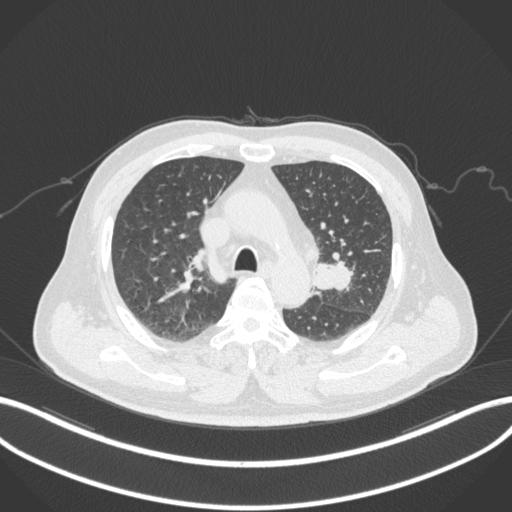
Chest CT, one axial slice. Slice 207 of 286 in the series (ordered by position). Reconstruction kernel B31f. 120 kVp. Lung window (W 1500 / L -600 HU). 1 mm slice thickness. 512 × 512 image matrix, field of view 400 × 400 mm. Male patient, age 67 years. Case-level facts recorded for this patient, not image findings: clinical TNM (as recorded): T2a N1 M0.
Structures marked on this image (bounding box drawn by a radiologist):
- lung tumour (recorded histology: adenocarcinoma): bounding box <311,261,352,294> (left, top, right, bottom; pixels)